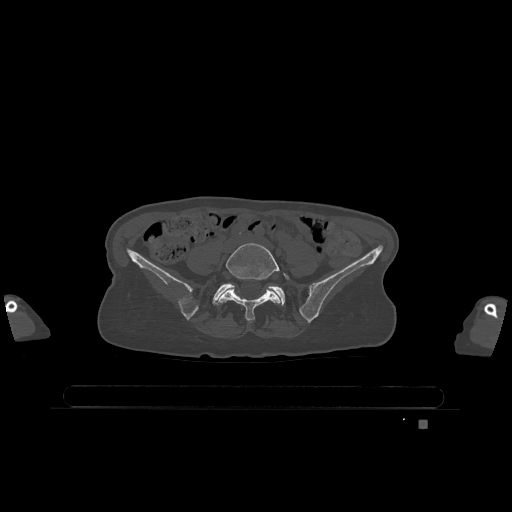
CT including the spine, one axial slice. Position 229 of 1317 along the scan axis. Bone window (W 1800 / L 400 HU). 0.5 mm slice thickness. 512 × 512 image matrix. Female patient, age 74 years. Case-level facts recorded for this patient, not image findings: primary cancer: lung; vertebrae with lytic lesions (as recorded): T1, T4, T5, T6, L4, L5.
Annotated regions visible in this slice (semi-automatically segmented with operator editing):
- L5 vertebra: bounding box <217,243,289,321> (left, top, right, bottom; pixels)